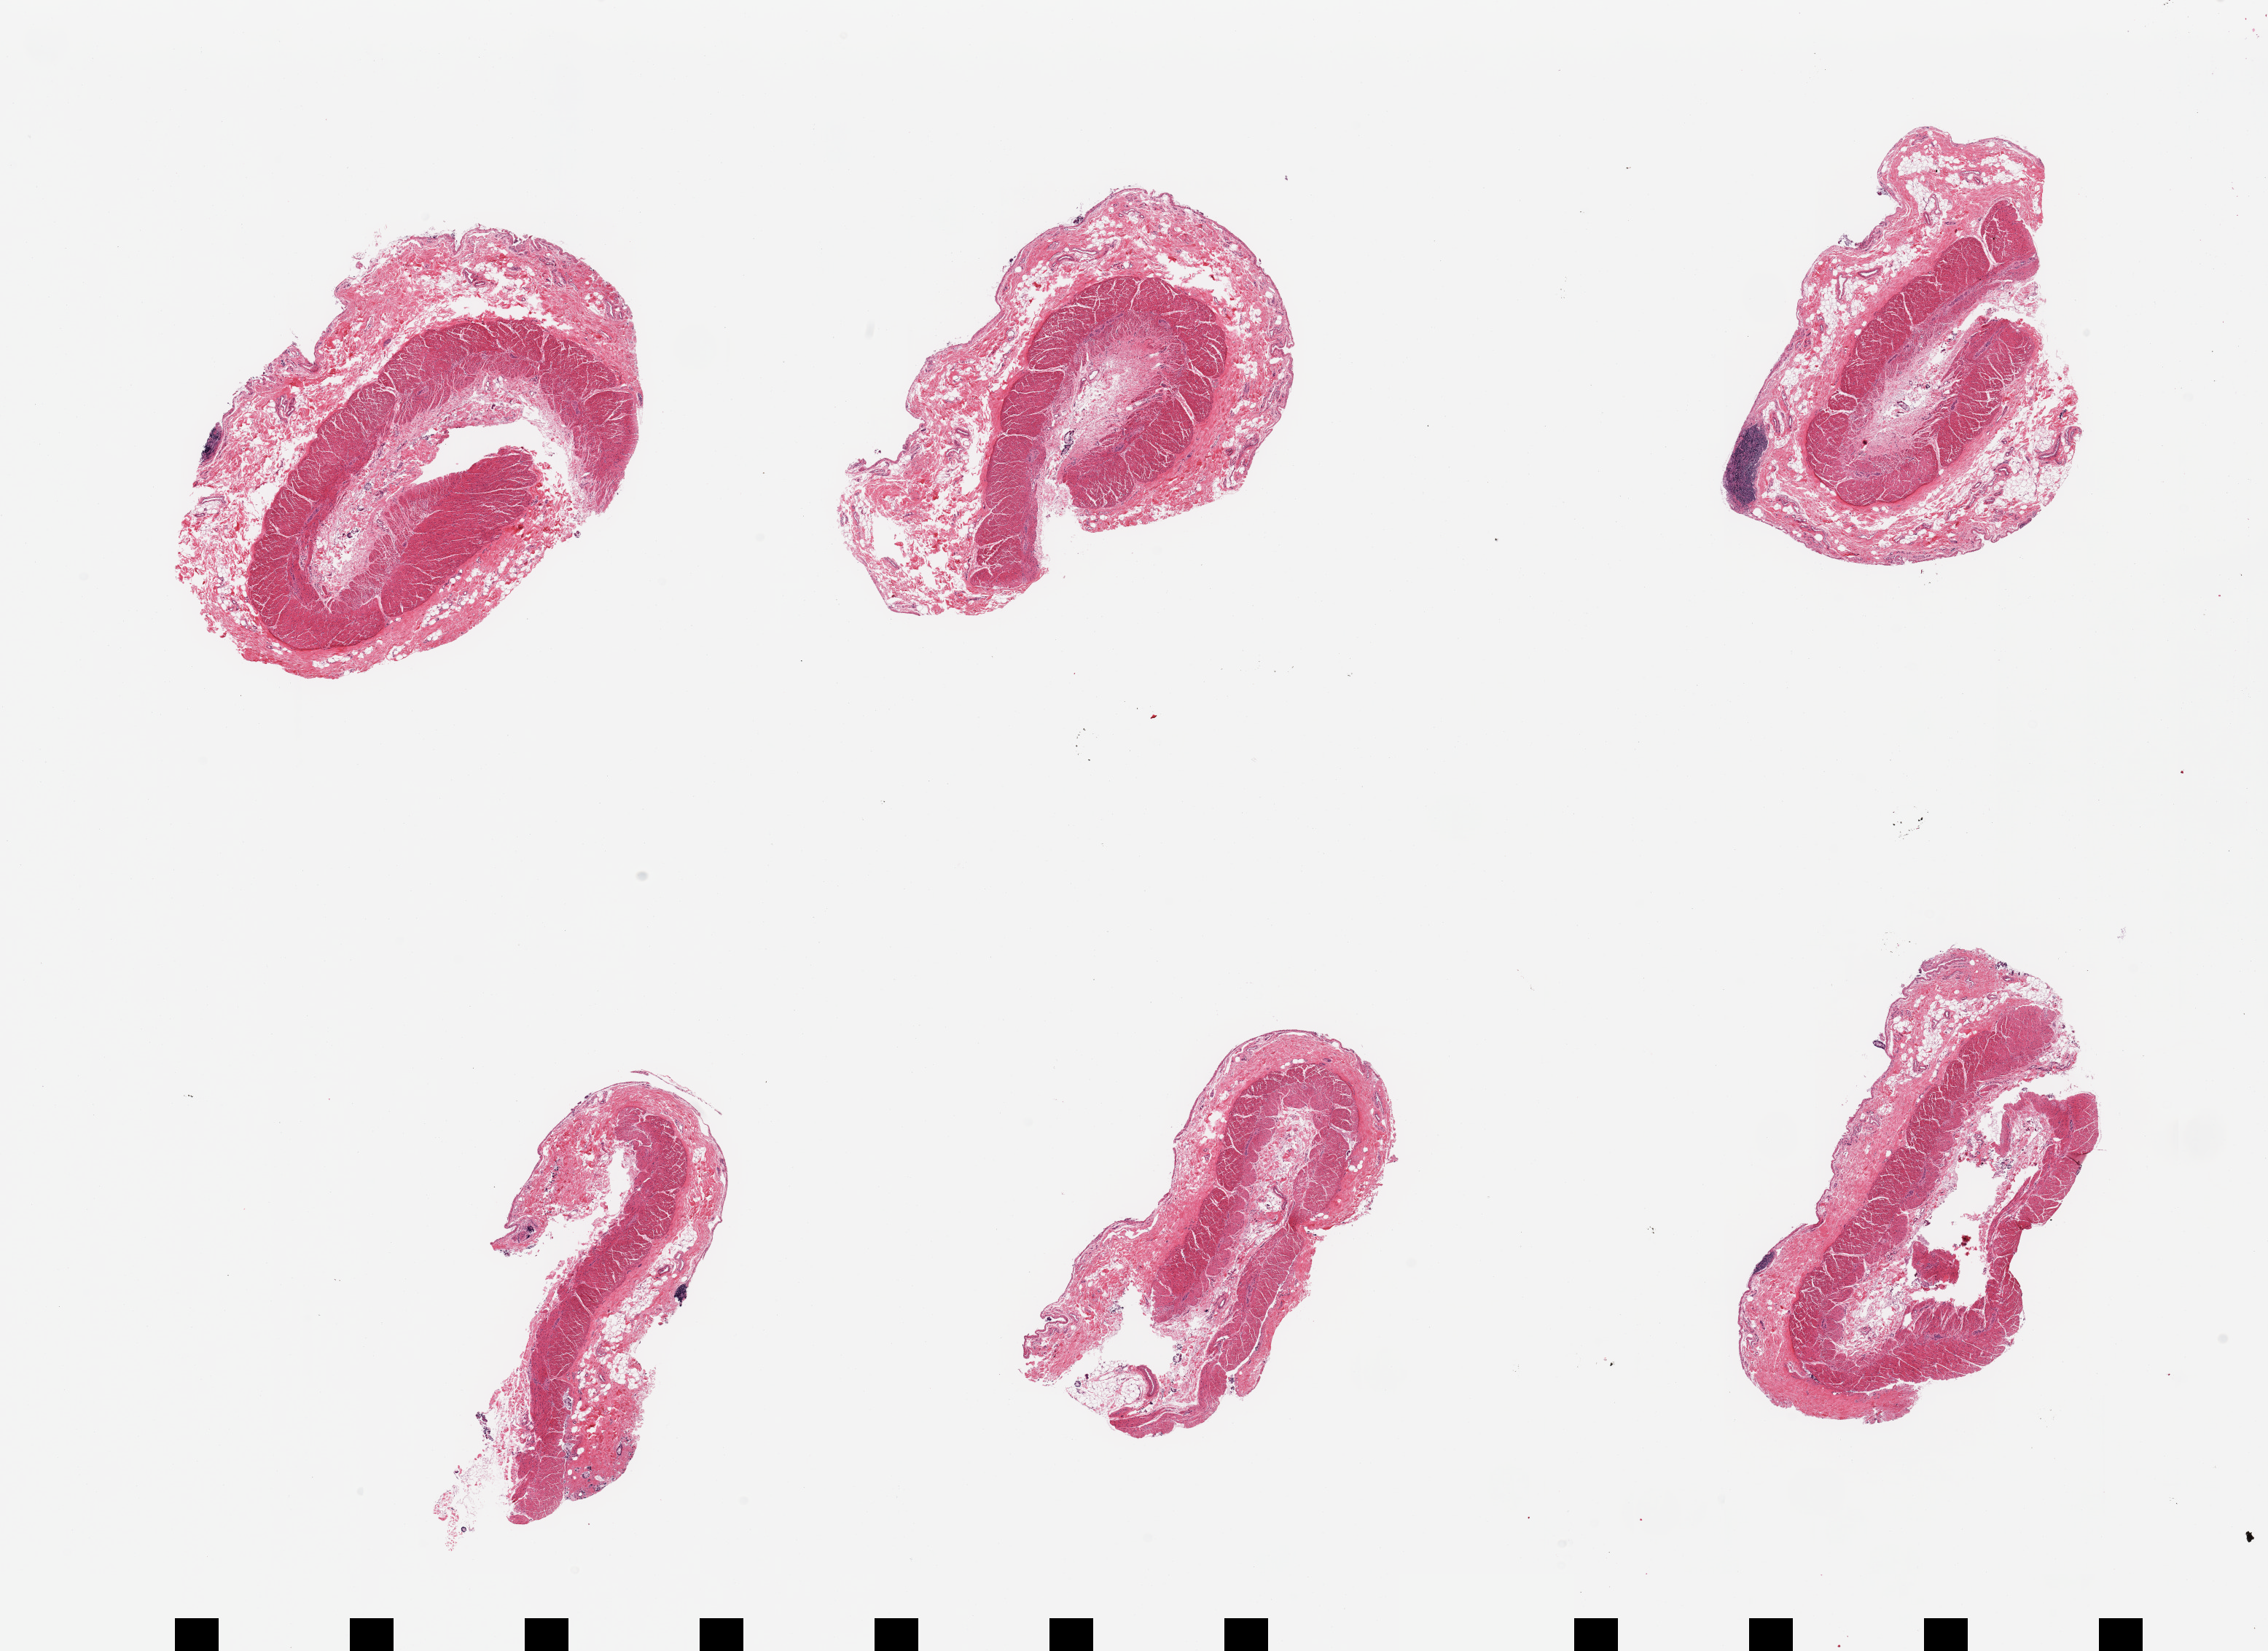
Haematoxylin and eosin whole-slide image — shown as a low-resolution overview of the whole scanned area (about 24.6 x 17.9 mm); PAXgene-fixed, paraffin-embedded tissue; sampled site (target tissue): transverse colon; donor tissue sample. Donor sex: male.
Pathologist's review note for this sample: 6 pieces, muscularis only; no target mucosa.